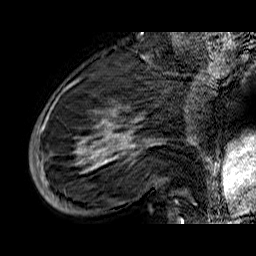
Breast MRI (dynamic contrast-enhanced), one sagittal slice. Slice 18 of 60 in the series (ordered by position). Dynamic contrast-enhanced series, time point 2 of 6 at this slice position (early post-contrast). 1.5 T. TE 6.5 ms, TR 32.9 ms. 4 mm slice thickness. 256 × 256 image matrix, field of view 200 × 200 mm. Female patient. Case-level facts recorded for this patient, not image findings: setting: breast cancer imaged before/during neoadjuvant chemotherapy; receptor status: HR-positive, HER2-negative.
Annotated regions visible in this slice (semi-automatic segmentation, software-assisted and operator-edited):
- analysis volume of interest (the breast-tissue region the enhancement analysis was run in; not a lesion): box from (x=33, y=74) to (x=176, y=210) px
- tumour enhancement mask (voxels above the 100 % enhancement threshold inside the analysis volume of interest): (x=35, y=100)–(x=163, y=195)